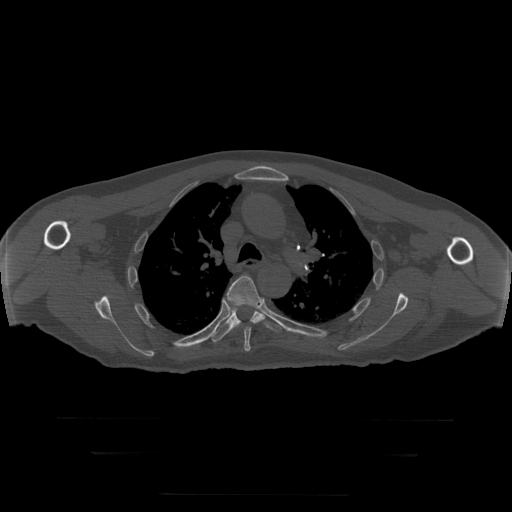
CT including the spine, one axial slice. Slice 217 of 397 in the series (ordered by position). Reconstruction kernel STANDARD. Bone window (W 1800 / L 400 HU). 1.25 mm slice thickness. 512 × 512 image matrix, field of view 510 × 510 mm. Patient age 73 years. From the clinical record (not read from this slice): primary cancer: prostate.
Annotated regions visible in this slice (semi-automatic segmentation, software-assisted and operator-edited):
- T5 vertebra: bounding box <227,276,265,352> (left, top, right, bottom; pixels)
- T6 vertebra: <208,298,282,343>